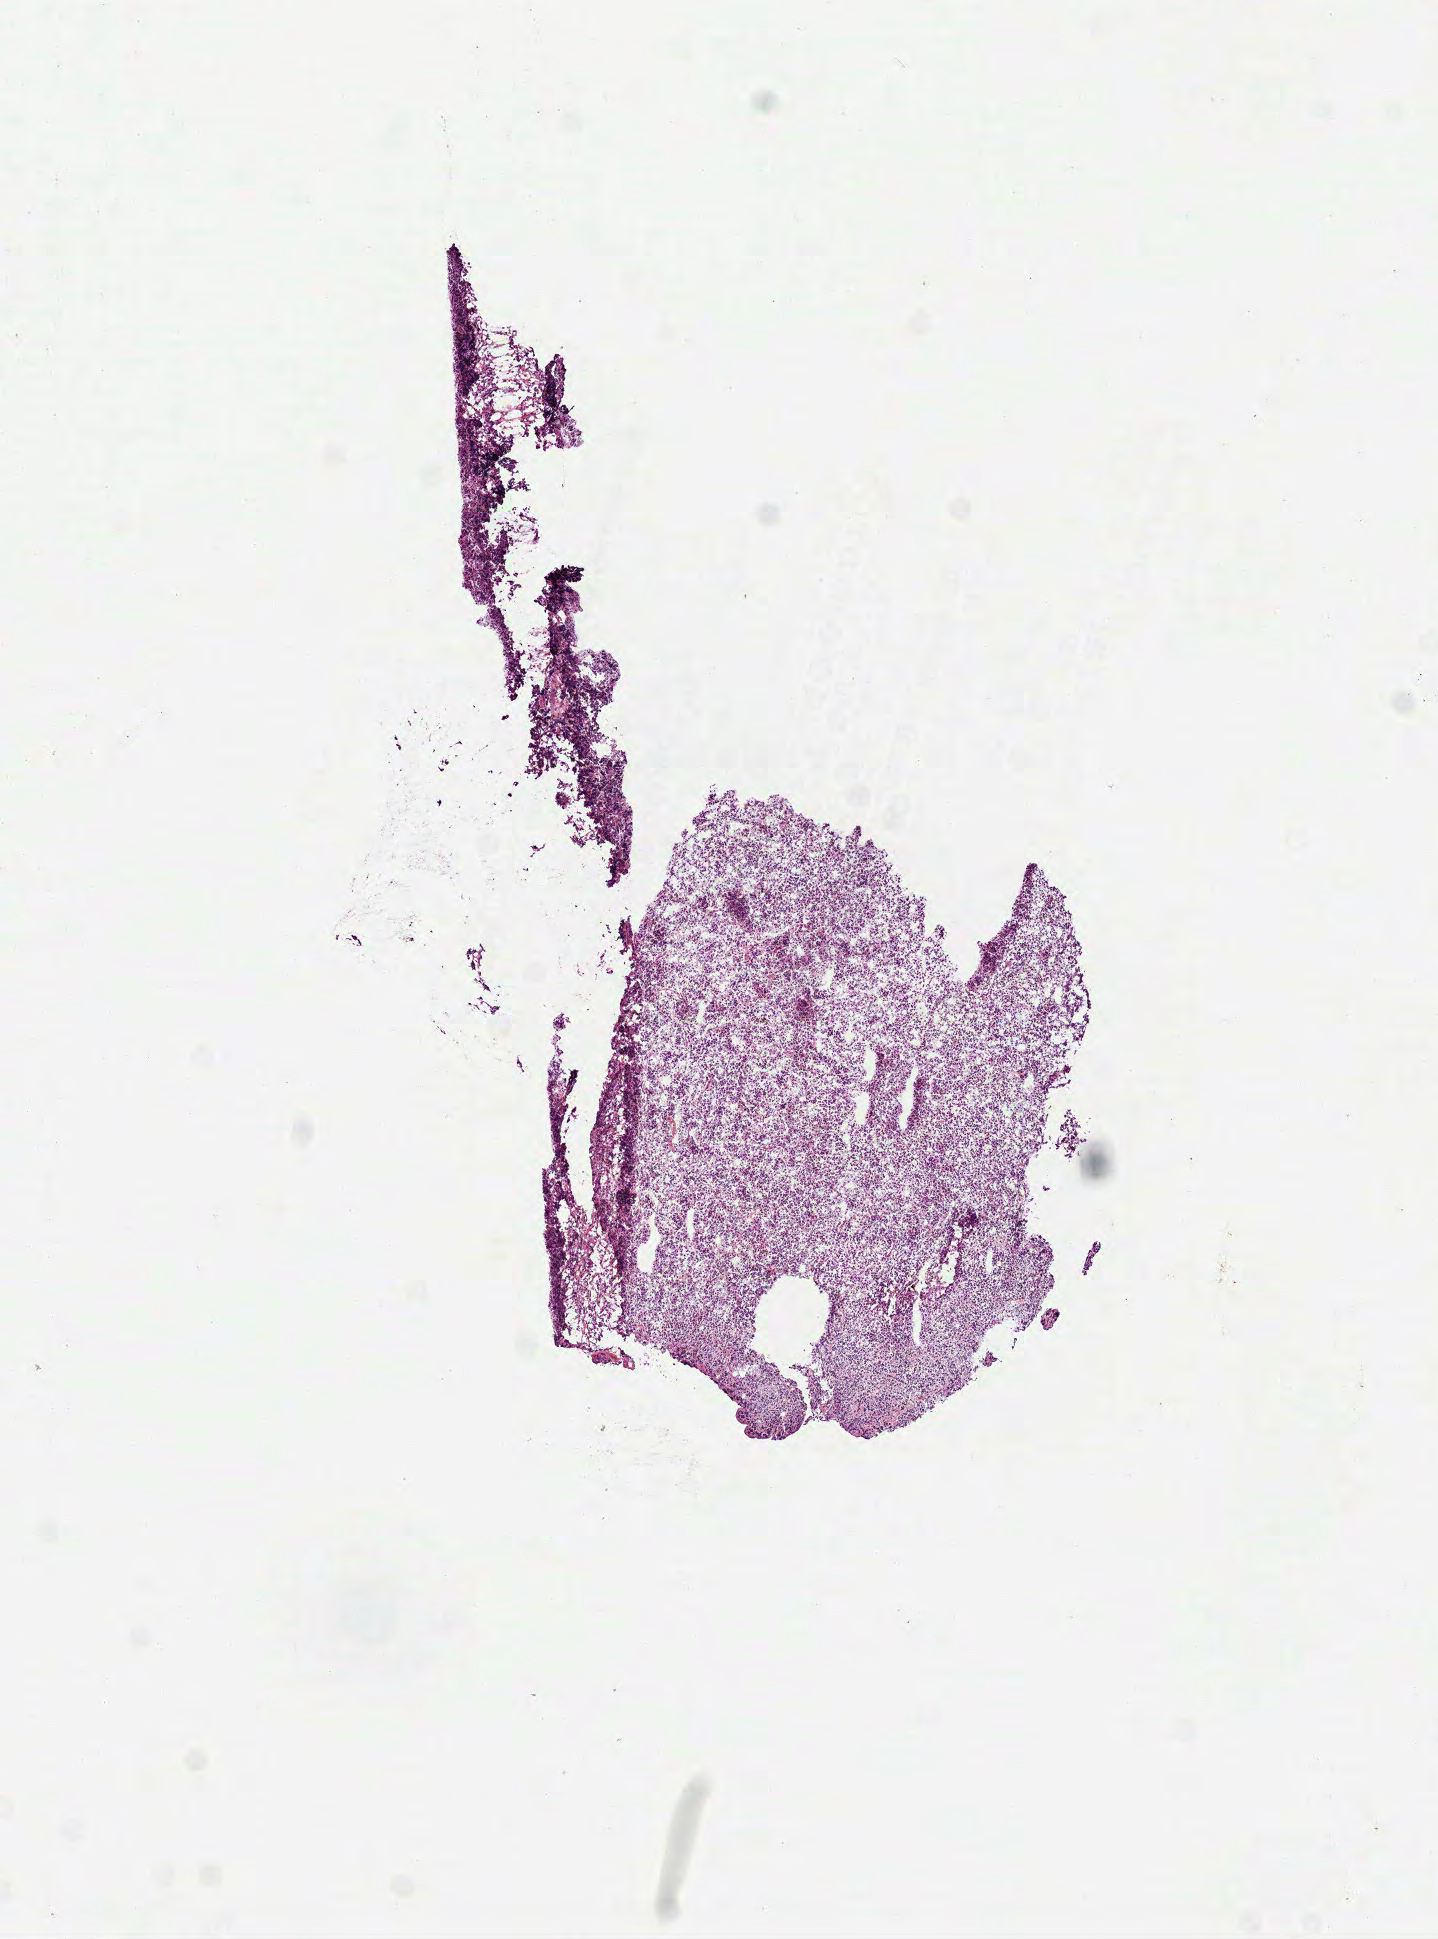
Digitized Hematoxylin and eosin (H&E) stained tissue section (whole slide), shown as a low-resolution overview of the whole scanned area (about 5.8 x 7.8 mm, acquisition: 40x scan). Frozen section from the top of the tissue portion. Lymphoid tissue, primary tumour sample. Female, age 57 years at initial diagnosis. Pathologist review of this section (percent, as recorded): tumour cells 100%, tumour nuclei 90%, normal cells 0%, stromal cells 0%, necrosis 0%. Inflammatory infiltration, as recorded: lymphocyte infiltration 90%.
Diagnosis: Diffuse large B-cell lymphoma, NOS.